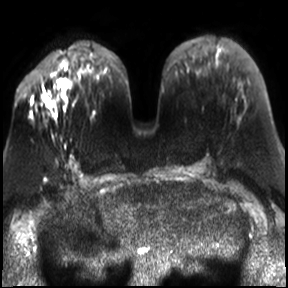
Breast MRI, one axial slice. Position 12 of 30 along the scan axis. Diffusion-weighted series; image 2 of 4 stored at this slice position (different b-values; order by instance number). 3 T. 288 × 288 image matrix, field of view 340 × 340 mm. Female patient.
Annotated regions visible in this slice (outlined manually by an expert reader):
- tumour on diffusion-weighted imaging: bounding box [x1, y1, x2, y2] px = [43, 78, 72, 107]